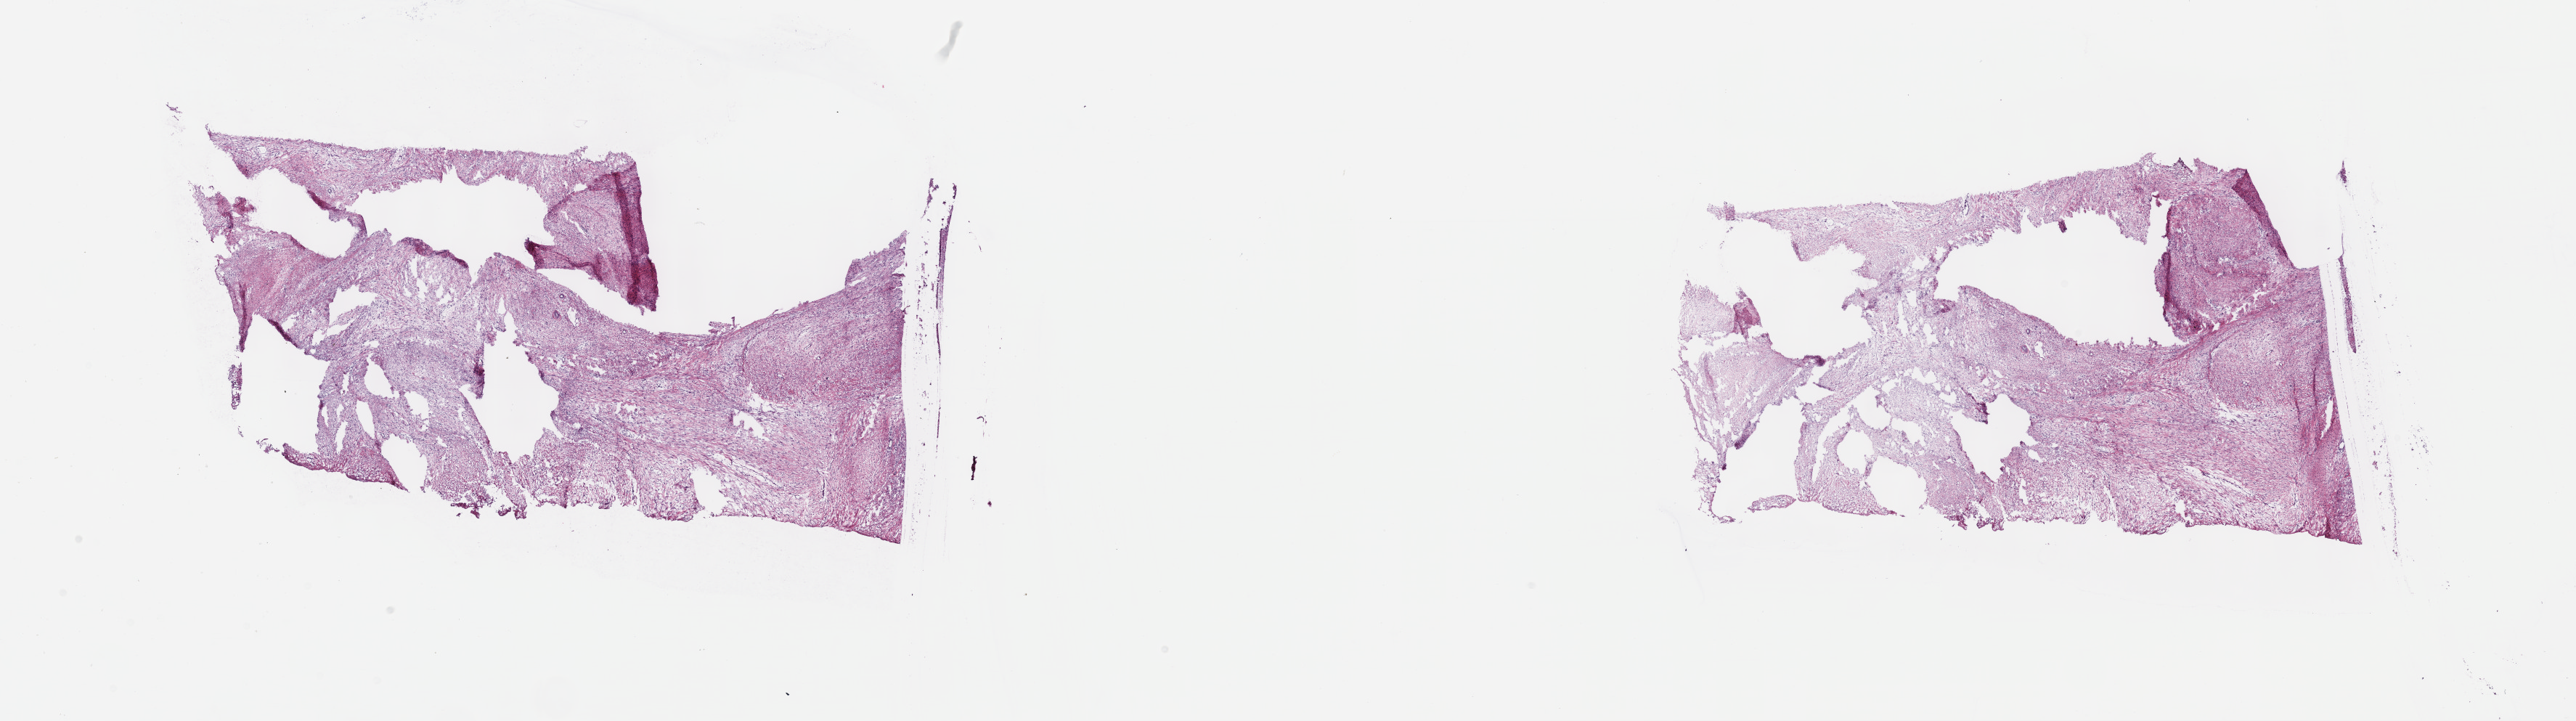
Hematoxylin and eosin (H&E) stained whole-slide image — shown as a low-resolution overview of the whole scanned area (about 28.7 x 8.0 mm). Frozen section. Connective, subcutaneous and other soft tissues, primary tumour sample. Female patient; age at initial diagnosis 24 years. Pathologist review of this section (percent, as recorded): tumour cells 100%, tumour nuclei 80%, normal cells 0%, stromal cells 0%, necrosis 0%. Infiltration values recorded for this section: lymphocyte infiltration 2%, monocyte infiltration 0%, neutrophil infiltration 0%.
- pathologic diagnosis: Aggressive fibromatosis (connective, subcutaneous and other soft tissues of thorax)